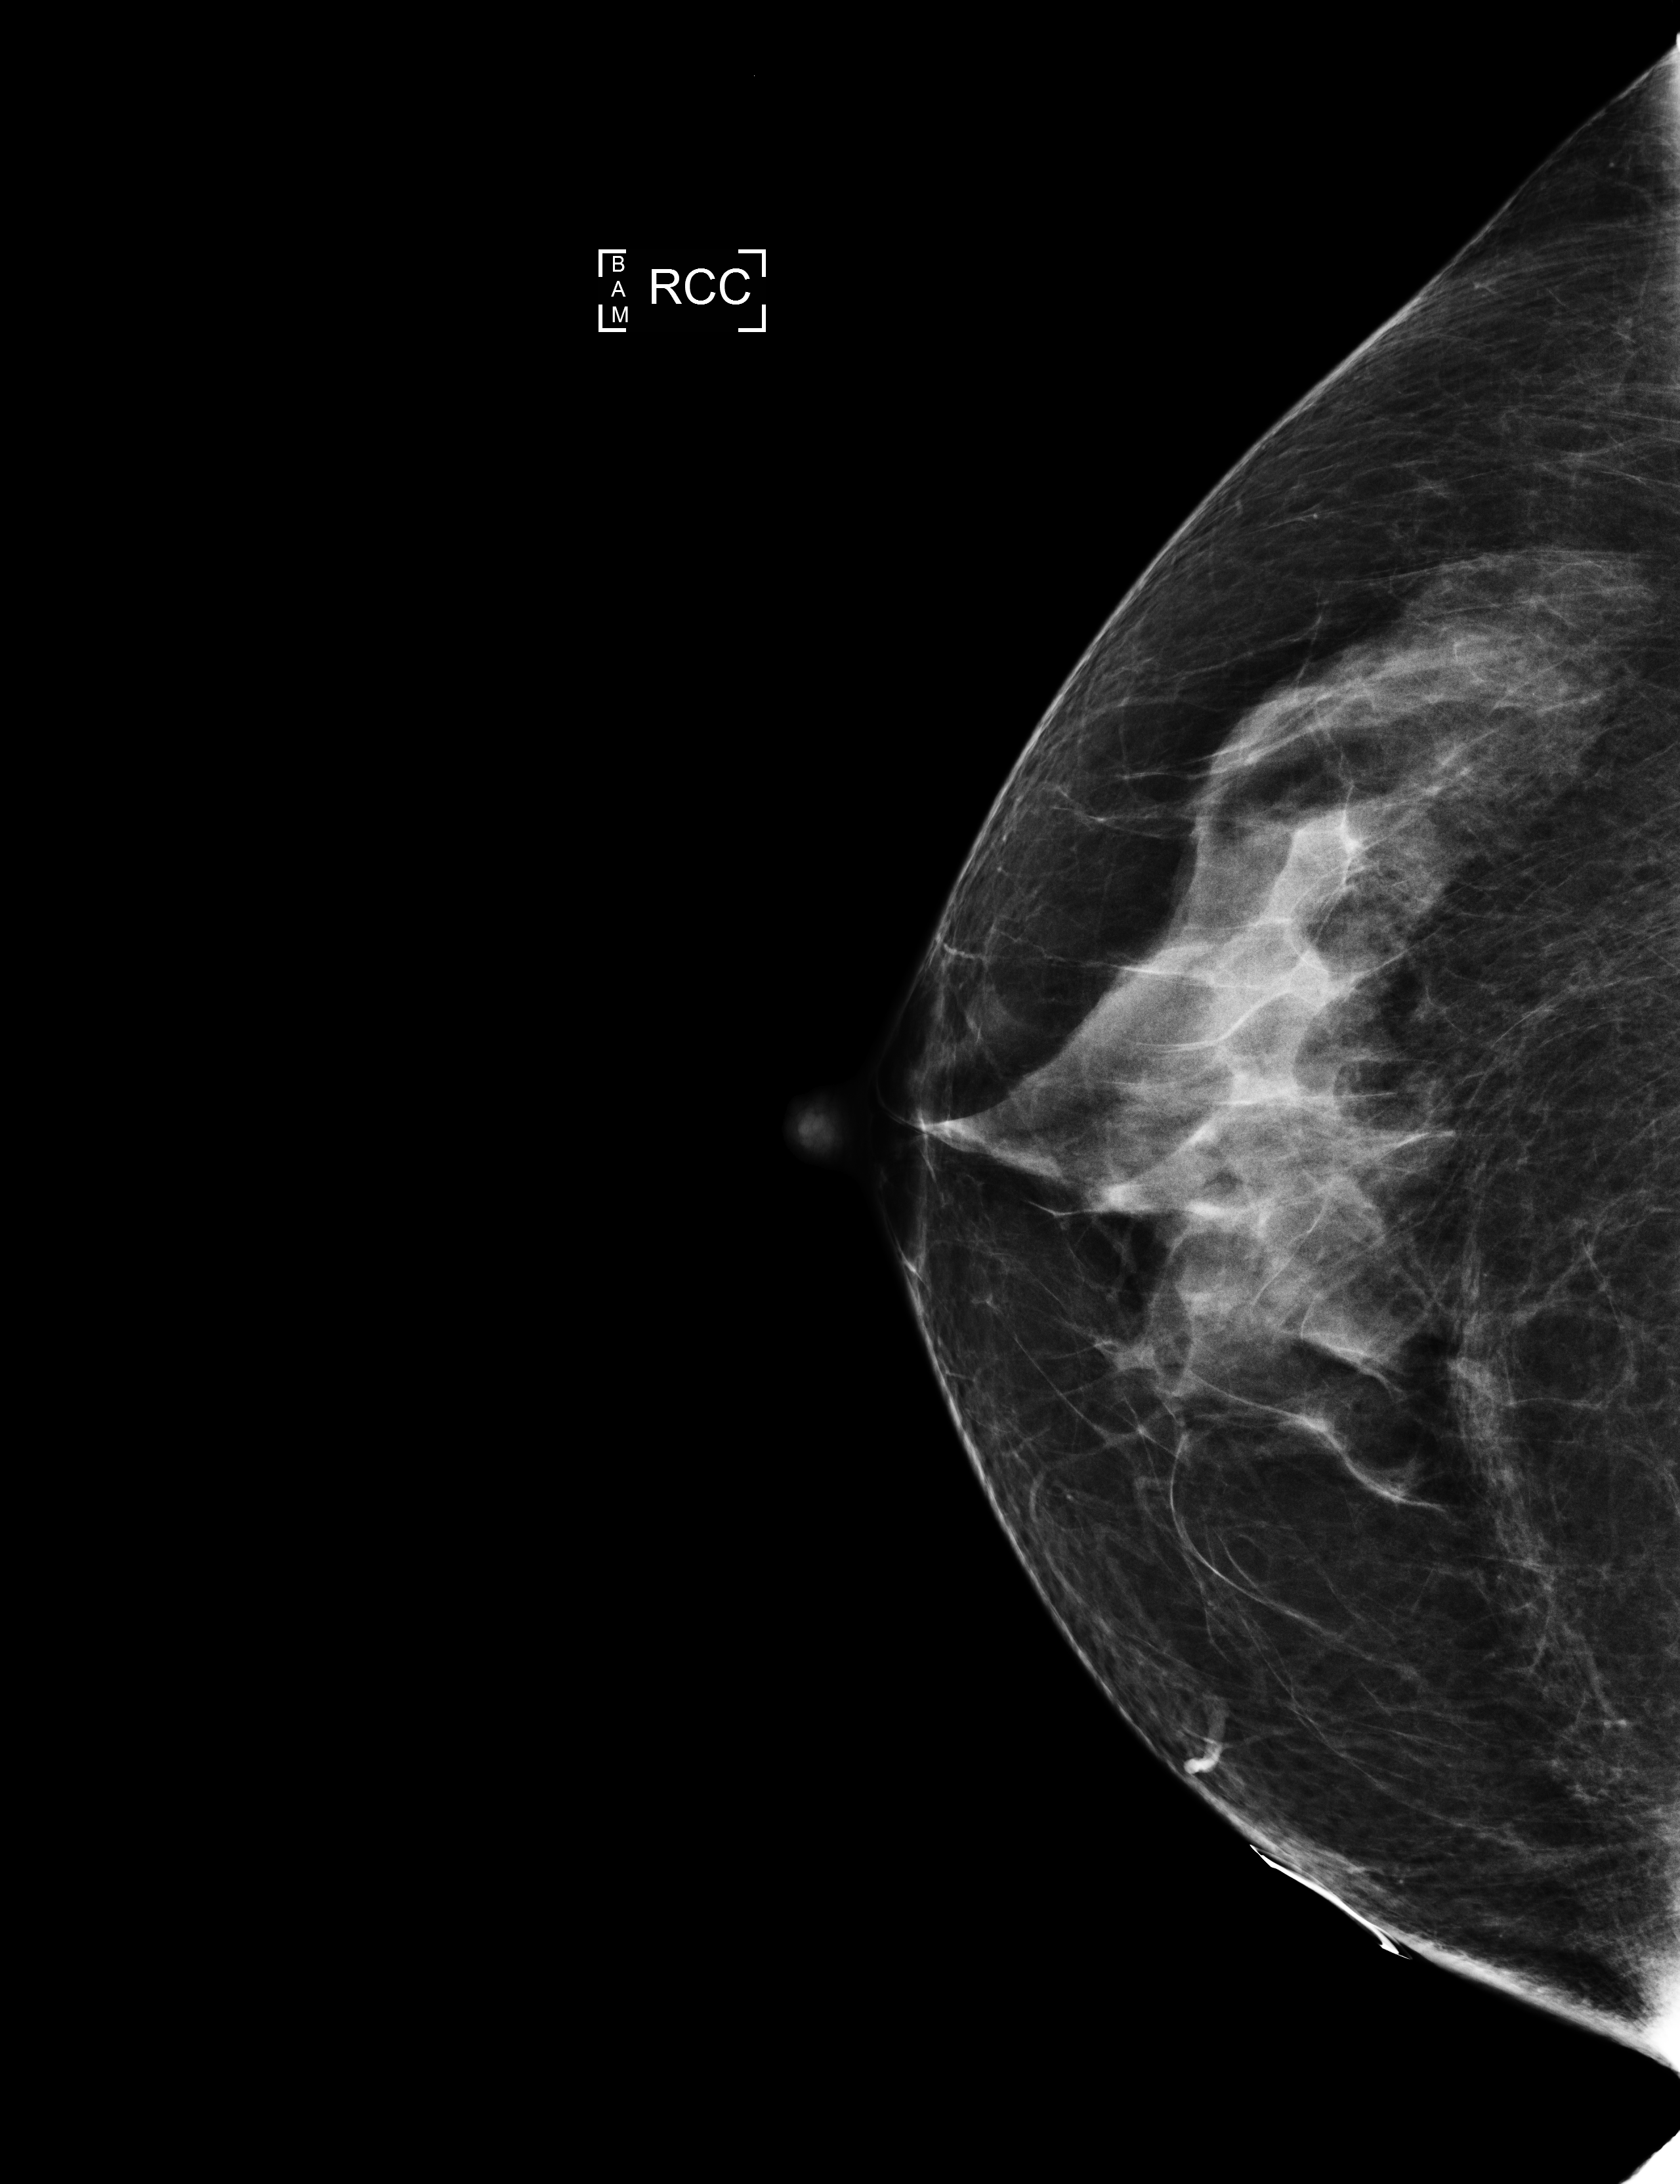
Annual screening mammography examination. Patient: female, 60 years.
Image type: full-field digital mammogram. Breast: right. Projection: CC view.